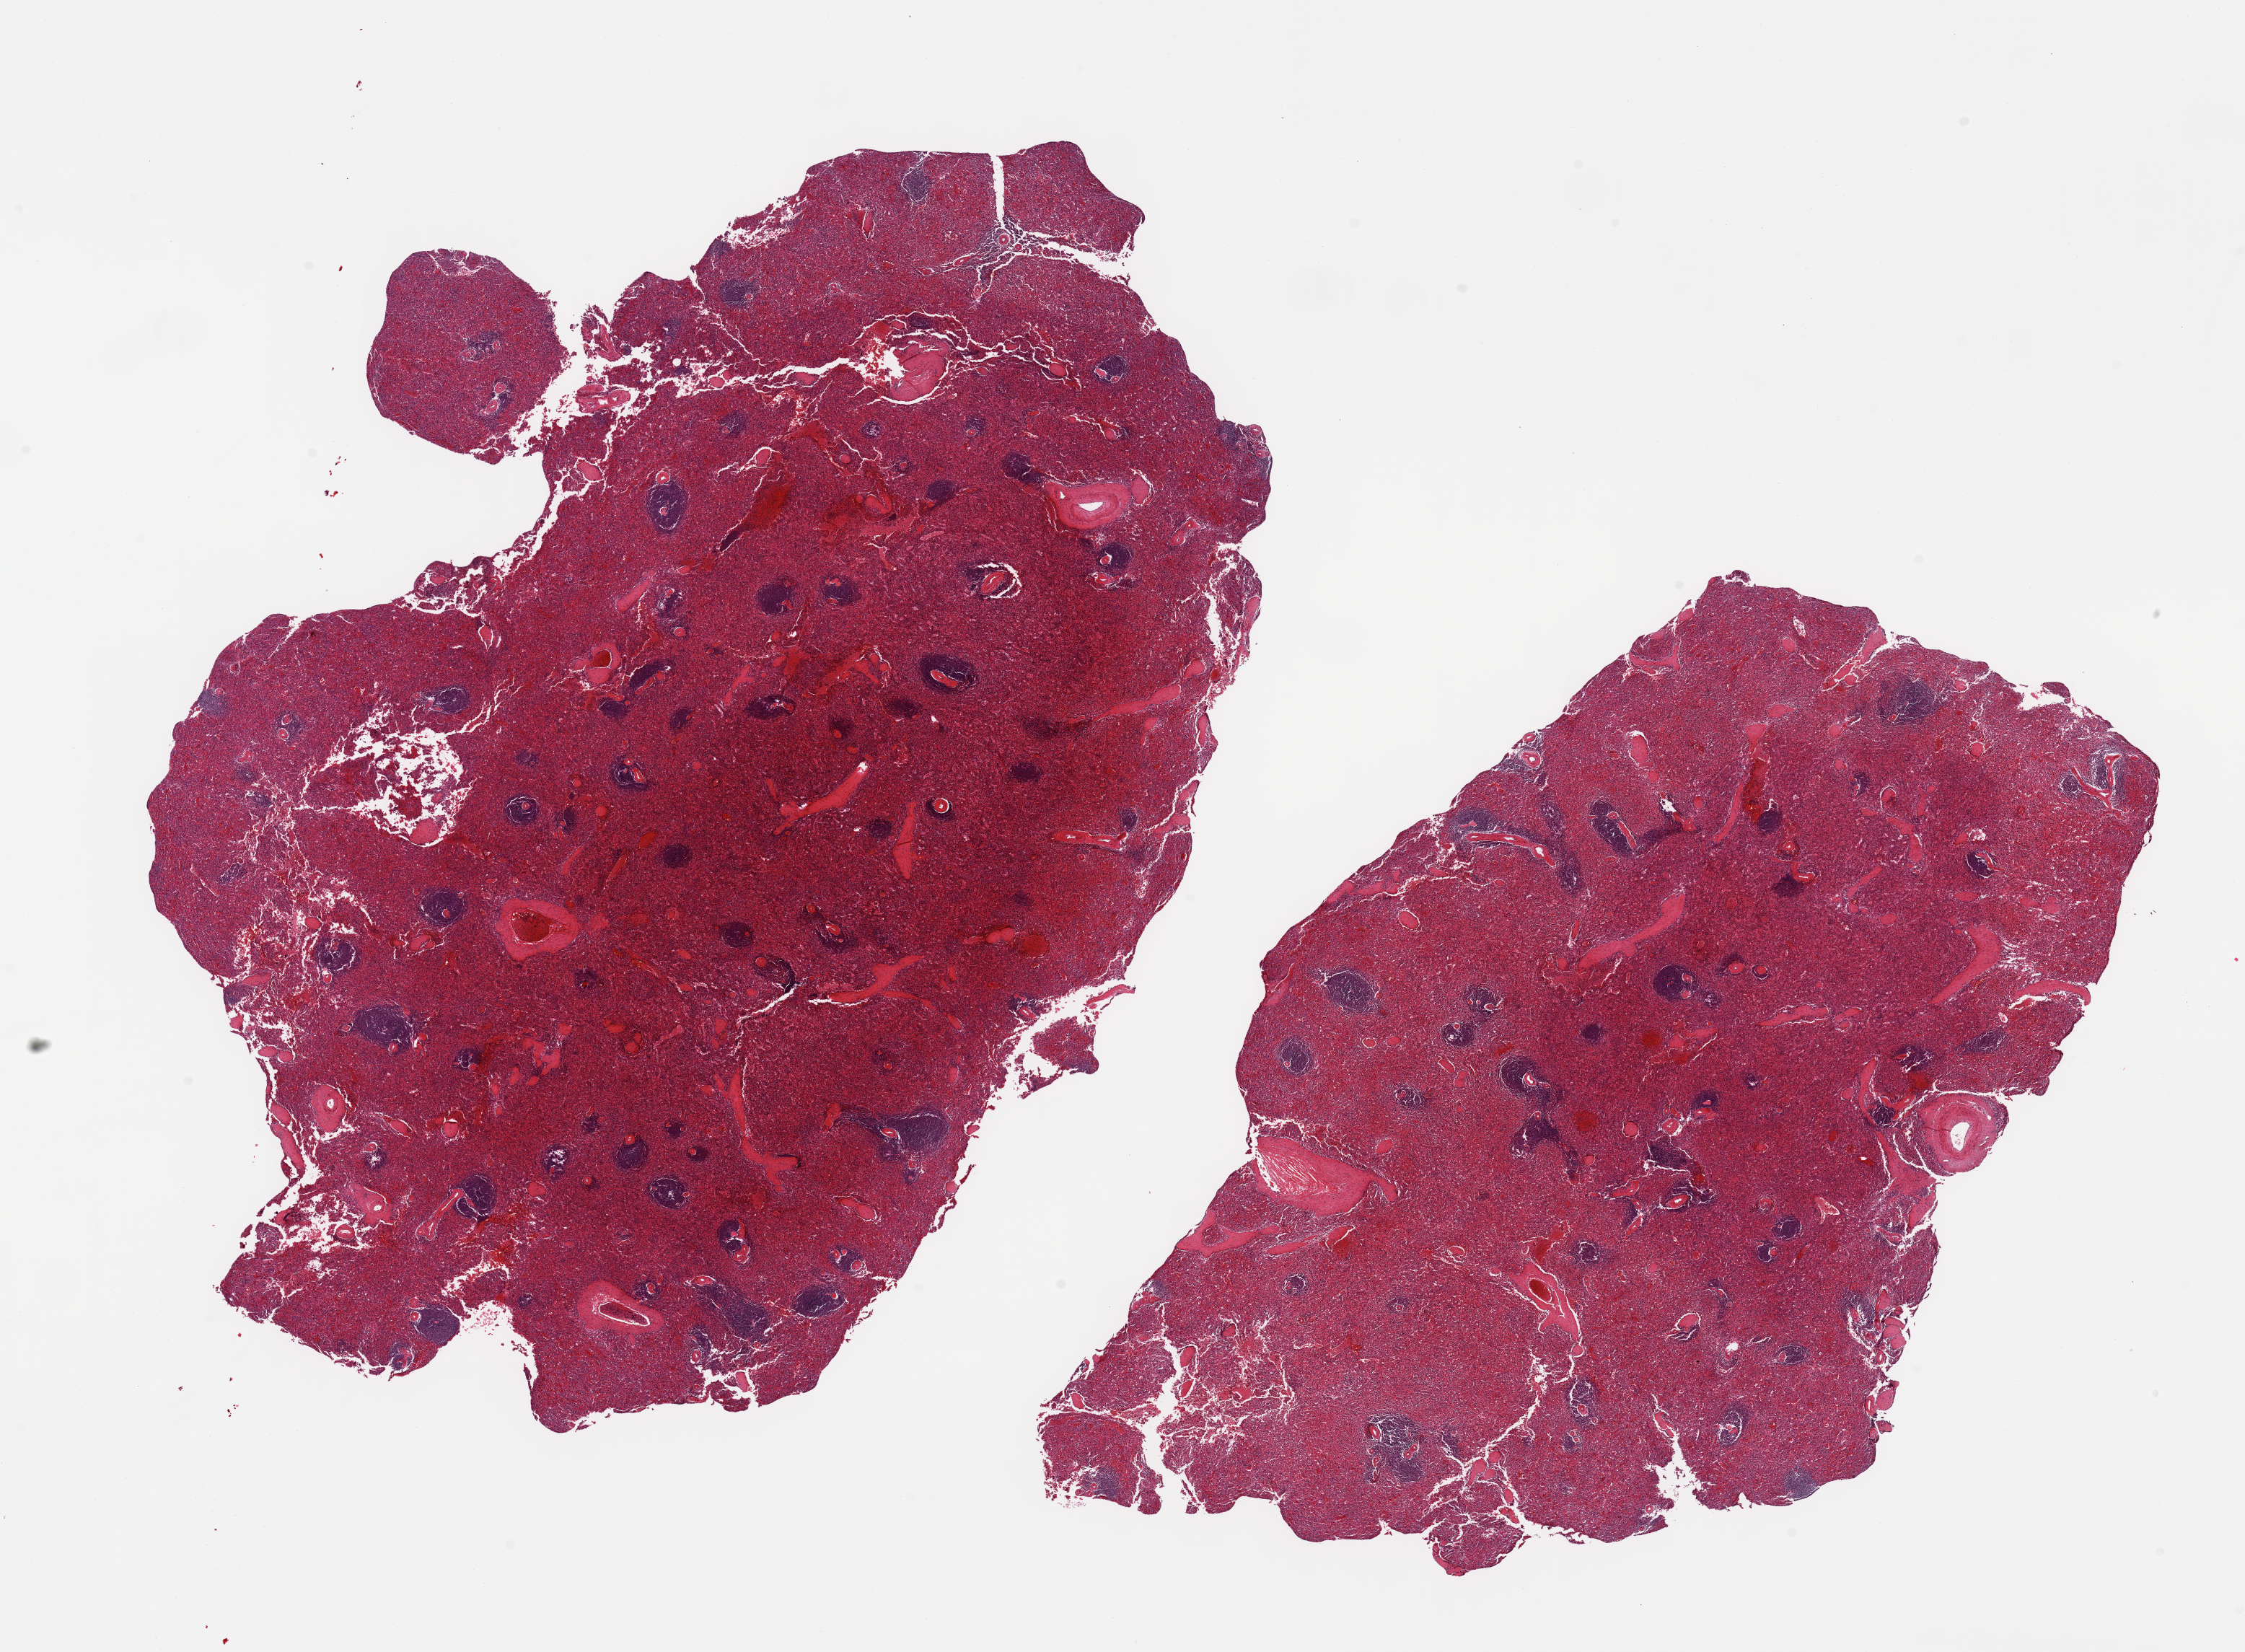
Digitized haematoxylin and eosin-stained section, whole scanned area (about 24.6 x 18.1 mm) shown as a low-resolution overview; PAXgene-fixed, paraffin-embedded tissue; section of spleen (target tissue); donor tissue sample. Donor: male.
Review note (as recorded): 2 partly fragmented pieces; moderately congested.